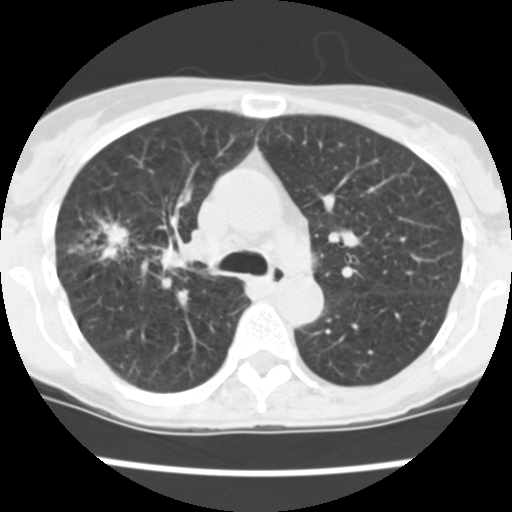
Low-dose screening chest CT, one axial slice; slice 162 of 252 in the series (ordered by position); lung window (W 1500 / L -600 HU); 2.5 mm slice thickness; 512 × 512 image matrix.
Annotated regions visible in this slice (manually delineated by an expert):
- lesion 2 (tumor, lower lobe of right lung): box from (x=91, y=219) to (x=129, y=260) px